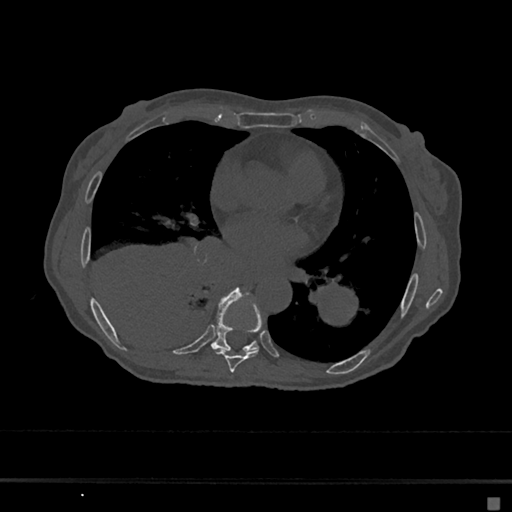
CT including the spine, one axial slice; slice 350 of 797 in the series (ordered by position); 120 kVp; bone window (W 1800 / L 400 HU); 0.5 mm slice thickness; 512 × 512 image matrix, field of view 360 × 360 mm. Female patient, age 68 years. Case-level facts recorded for this patient, not image findings: primary cancer: renal.
Annotated regions visible in this slice (semi-automatic segmentation, software-assisted and operator-edited):
- T7 vertebra: box from (x=216, y=301) to (x=263, y=373) px
- T8 vertebra: (x=211, y=289)–(x=258, y=353)